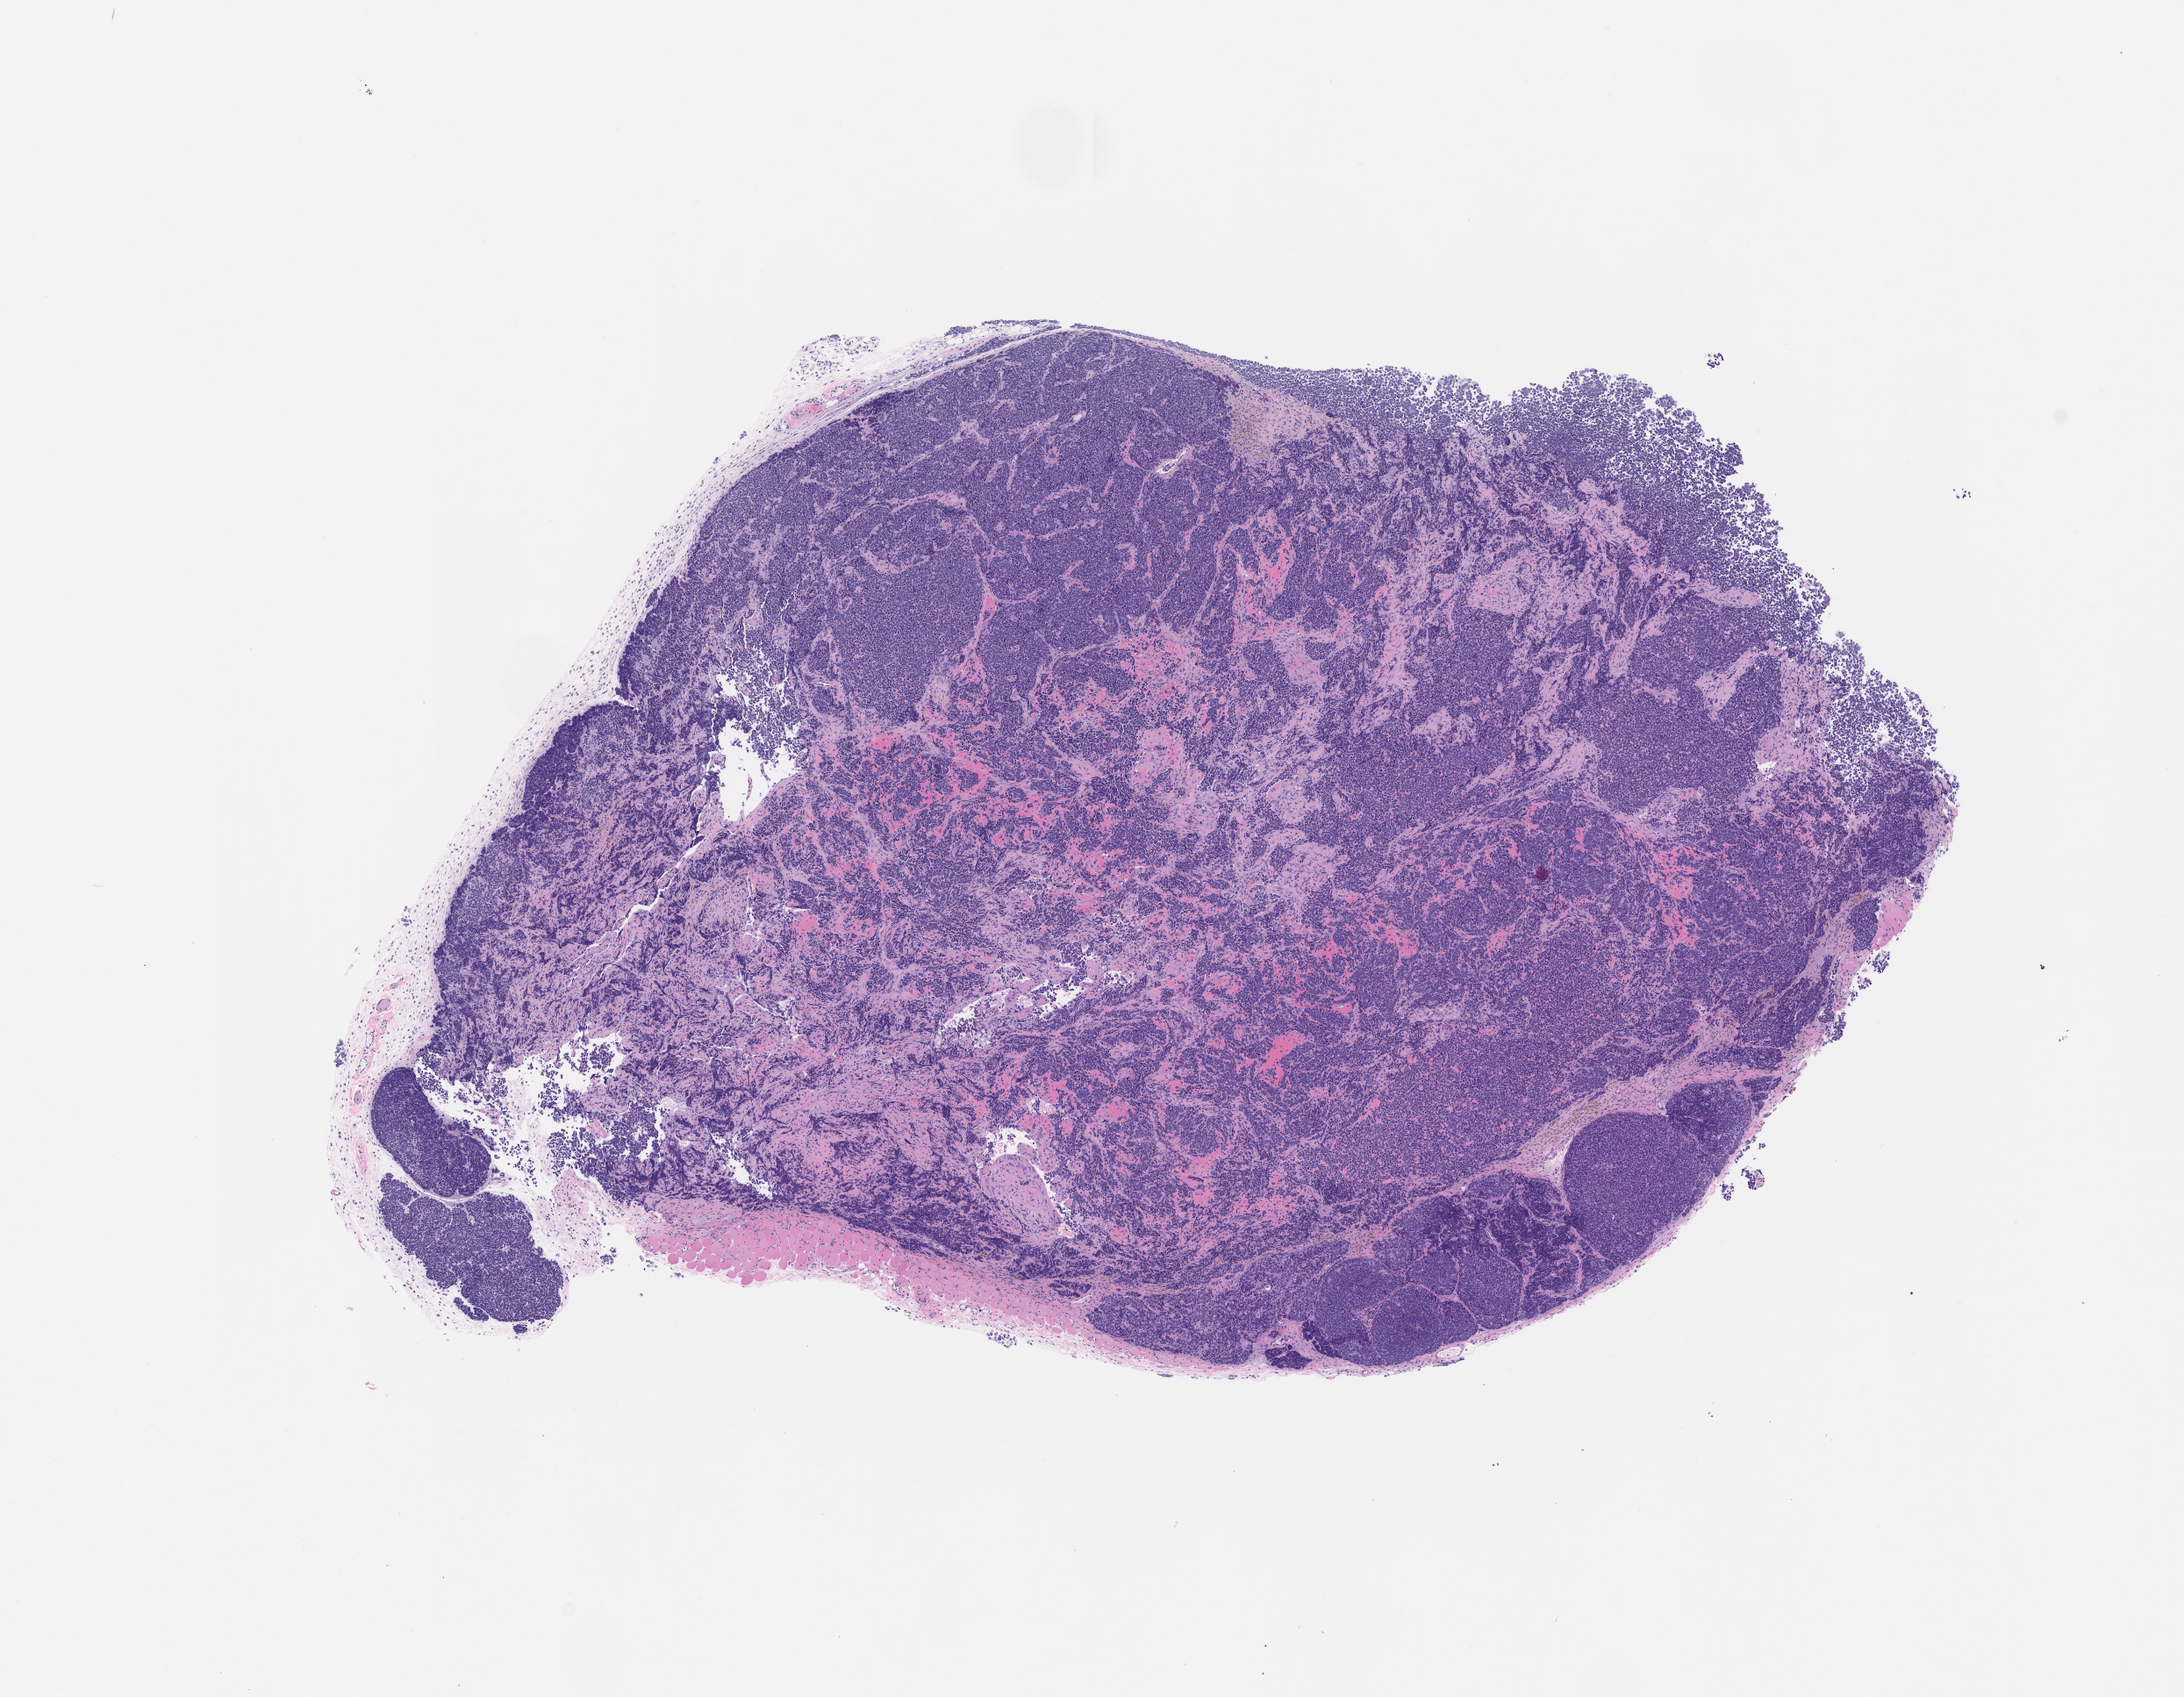
H&E whole-slide image of a patient-derived xenograft (PDX) tumor grown in a mouse, passage 0, shown as a low-resolution overview of the whole scanned area (about 10.0 x 7.7 mm), FFPE section, originating tumor site category: bladder.
• originating patient diagnosis: Bladder Small Cell Neuroendocrine Carcinoma